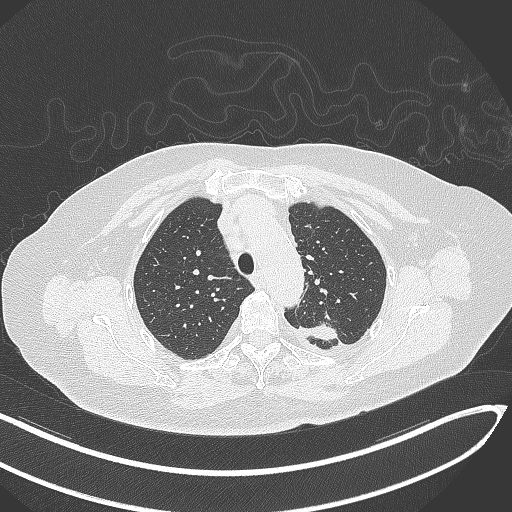
Chest CT, one axial slice; slice 244 of 270 in the series (ordered by position); lung window (W 1500 / L -600 HU); 1 mm slice thickness; 512 × 512 image matrix, field of view 400 × 400 mm. Patient: female, 76 years. From the clinical record (not read from this slice): clinical TNM (as recorded): T1c N0 M0.
Annotated regions visible in this slice (rectangle marked by the reading radiologist):
- lung tumour (recorded histology: adenocarcinoma): bounding box [x1, y1, x2, y2] px = [301, 323, 337, 343]